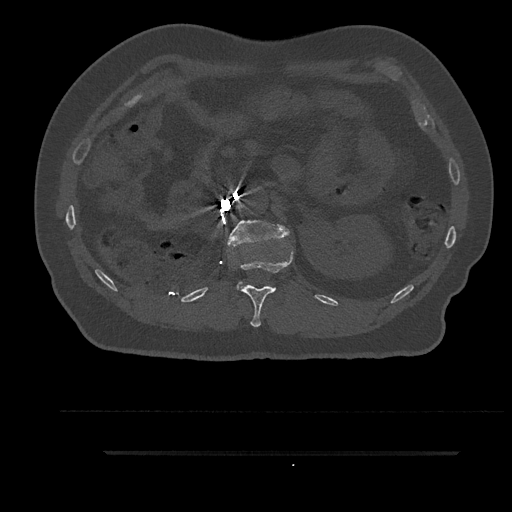
CT including the spine, one axial slice. Slice 216 of 797 in the series (ordered by position). 120 kVp. Bone window (W 1800 / L 400 HU). 0.5 mm slice thickness. 512 × 512 image matrix. Male patient, age 63 years. From the clinical record (not read from this slice): primary cancer: renal; vertebrae with lytic lesions (as recorded): T8.
Structures marked on this image (semi-automatic segmentation, software-assisted and operator-edited):
- L1 vertebra: bounding box (x1, y1, x2, y2) in pixels: (227, 220, 290, 289)
- T12 vertebra: (239, 250, 293, 327)